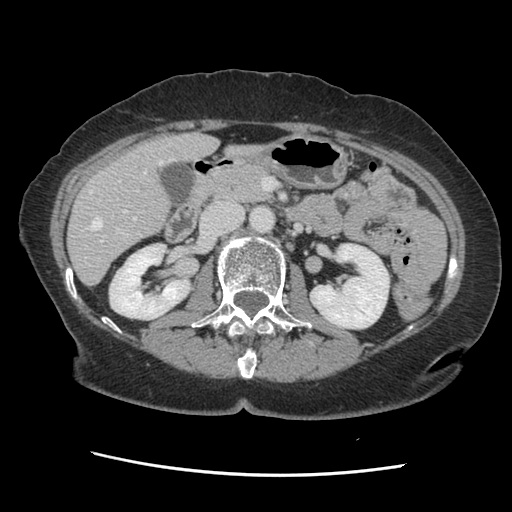
Contrast-enhanced abdominal CT, one axial slice. Slice 64 of 141 in the series (ordered by position). Soft-tissue window (W 400 / L 40 HU). 2.5 mm slice thickness. 512 × 512 image matrix, field of view 330 × 330 mm. Female patient, age 61 years. Case-level facts recorded for this patient, not image findings: diagnosis: colorectal cancer liver metastases, imaged before liver resection; multiple liver metastases: no; largest metastasis: 2.4 cm; chemotherapy before resection: no.
Structures marked on this image (outlined manually by an expert reader):
- hepatic veins: bounding box [x1, y1, x2, y2] px = [87, 158, 173, 230]
- liver: [69, 134, 258, 284]
- planned liver remnant (the part of the liver to remain after resection): [69, 134, 258, 284]
- portal vein (with intrahepatic branches): [100, 180, 138, 242]